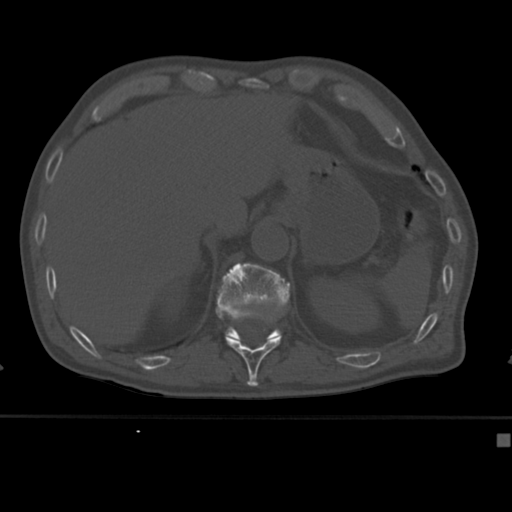
CT including the spine, one axial slice; slice 202 of 430 in the series (ordered by position); reconstruction kernel Br40s; 120 kVp; bone window (W 1800 / L 400 HU); 1.5 mm slice thickness; 512 × 512 image matrix, field of view 337 × 337 mm. Patient: male, 64 years. From the clinical record (not read from this slice): primary cancer: uterus; vertebrae with lytic lesions (as recorded): T1, T4, T5, T7, L5.
Structures marked on this image (semi-automatically segmented with operator editing):
- T11 vertebra: bounding box (x1, y1, x2, y2) in pixels: (225, 314, 281, 382)
- T12 vertebra: (216, 263, 290, 339)